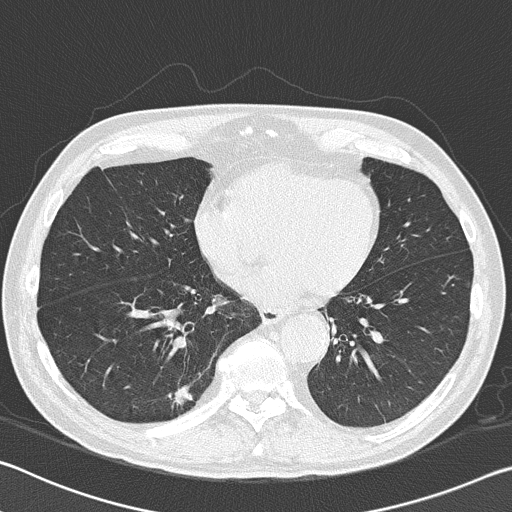
Chest CT (low-dose screening protocol), one axial image. First (baseline) screen. Lung window (W 1500 / L -600 HU). 2 mm slice thickness. 120 kVp. 512 × 512 image matrix, field of view 340 × 340 mm. Male, age 74 years at enrolment.
- Lesion marked by an expert reader, bounding box [x1, y1, x2, y2] px = [148, 367, 215, 427].
- Screening reader's record for this exam (one nodule recorded; not confirmed to be the boxed lesion): non-calcified nodule or mass ≥4 mm, right lower lobe, 13 × 11 mm, spiculated (stellate) margins, soft tissue attenuation.
- Official screen result: positive, change unspecified: nodule(s) >= 4 mm or enlarging nodule(s), mass(es), or other non-specific abnormalities suspicious for lung cancer.
- Participant outcome: lung cancer diagnosed 414 days after this screen — bronchiolo-alveolar adenocarcinoma, NOS, right lower lobe, moderately differentiated (G2), stage IA (AJCC 6th edition), 16 mm at pathology.